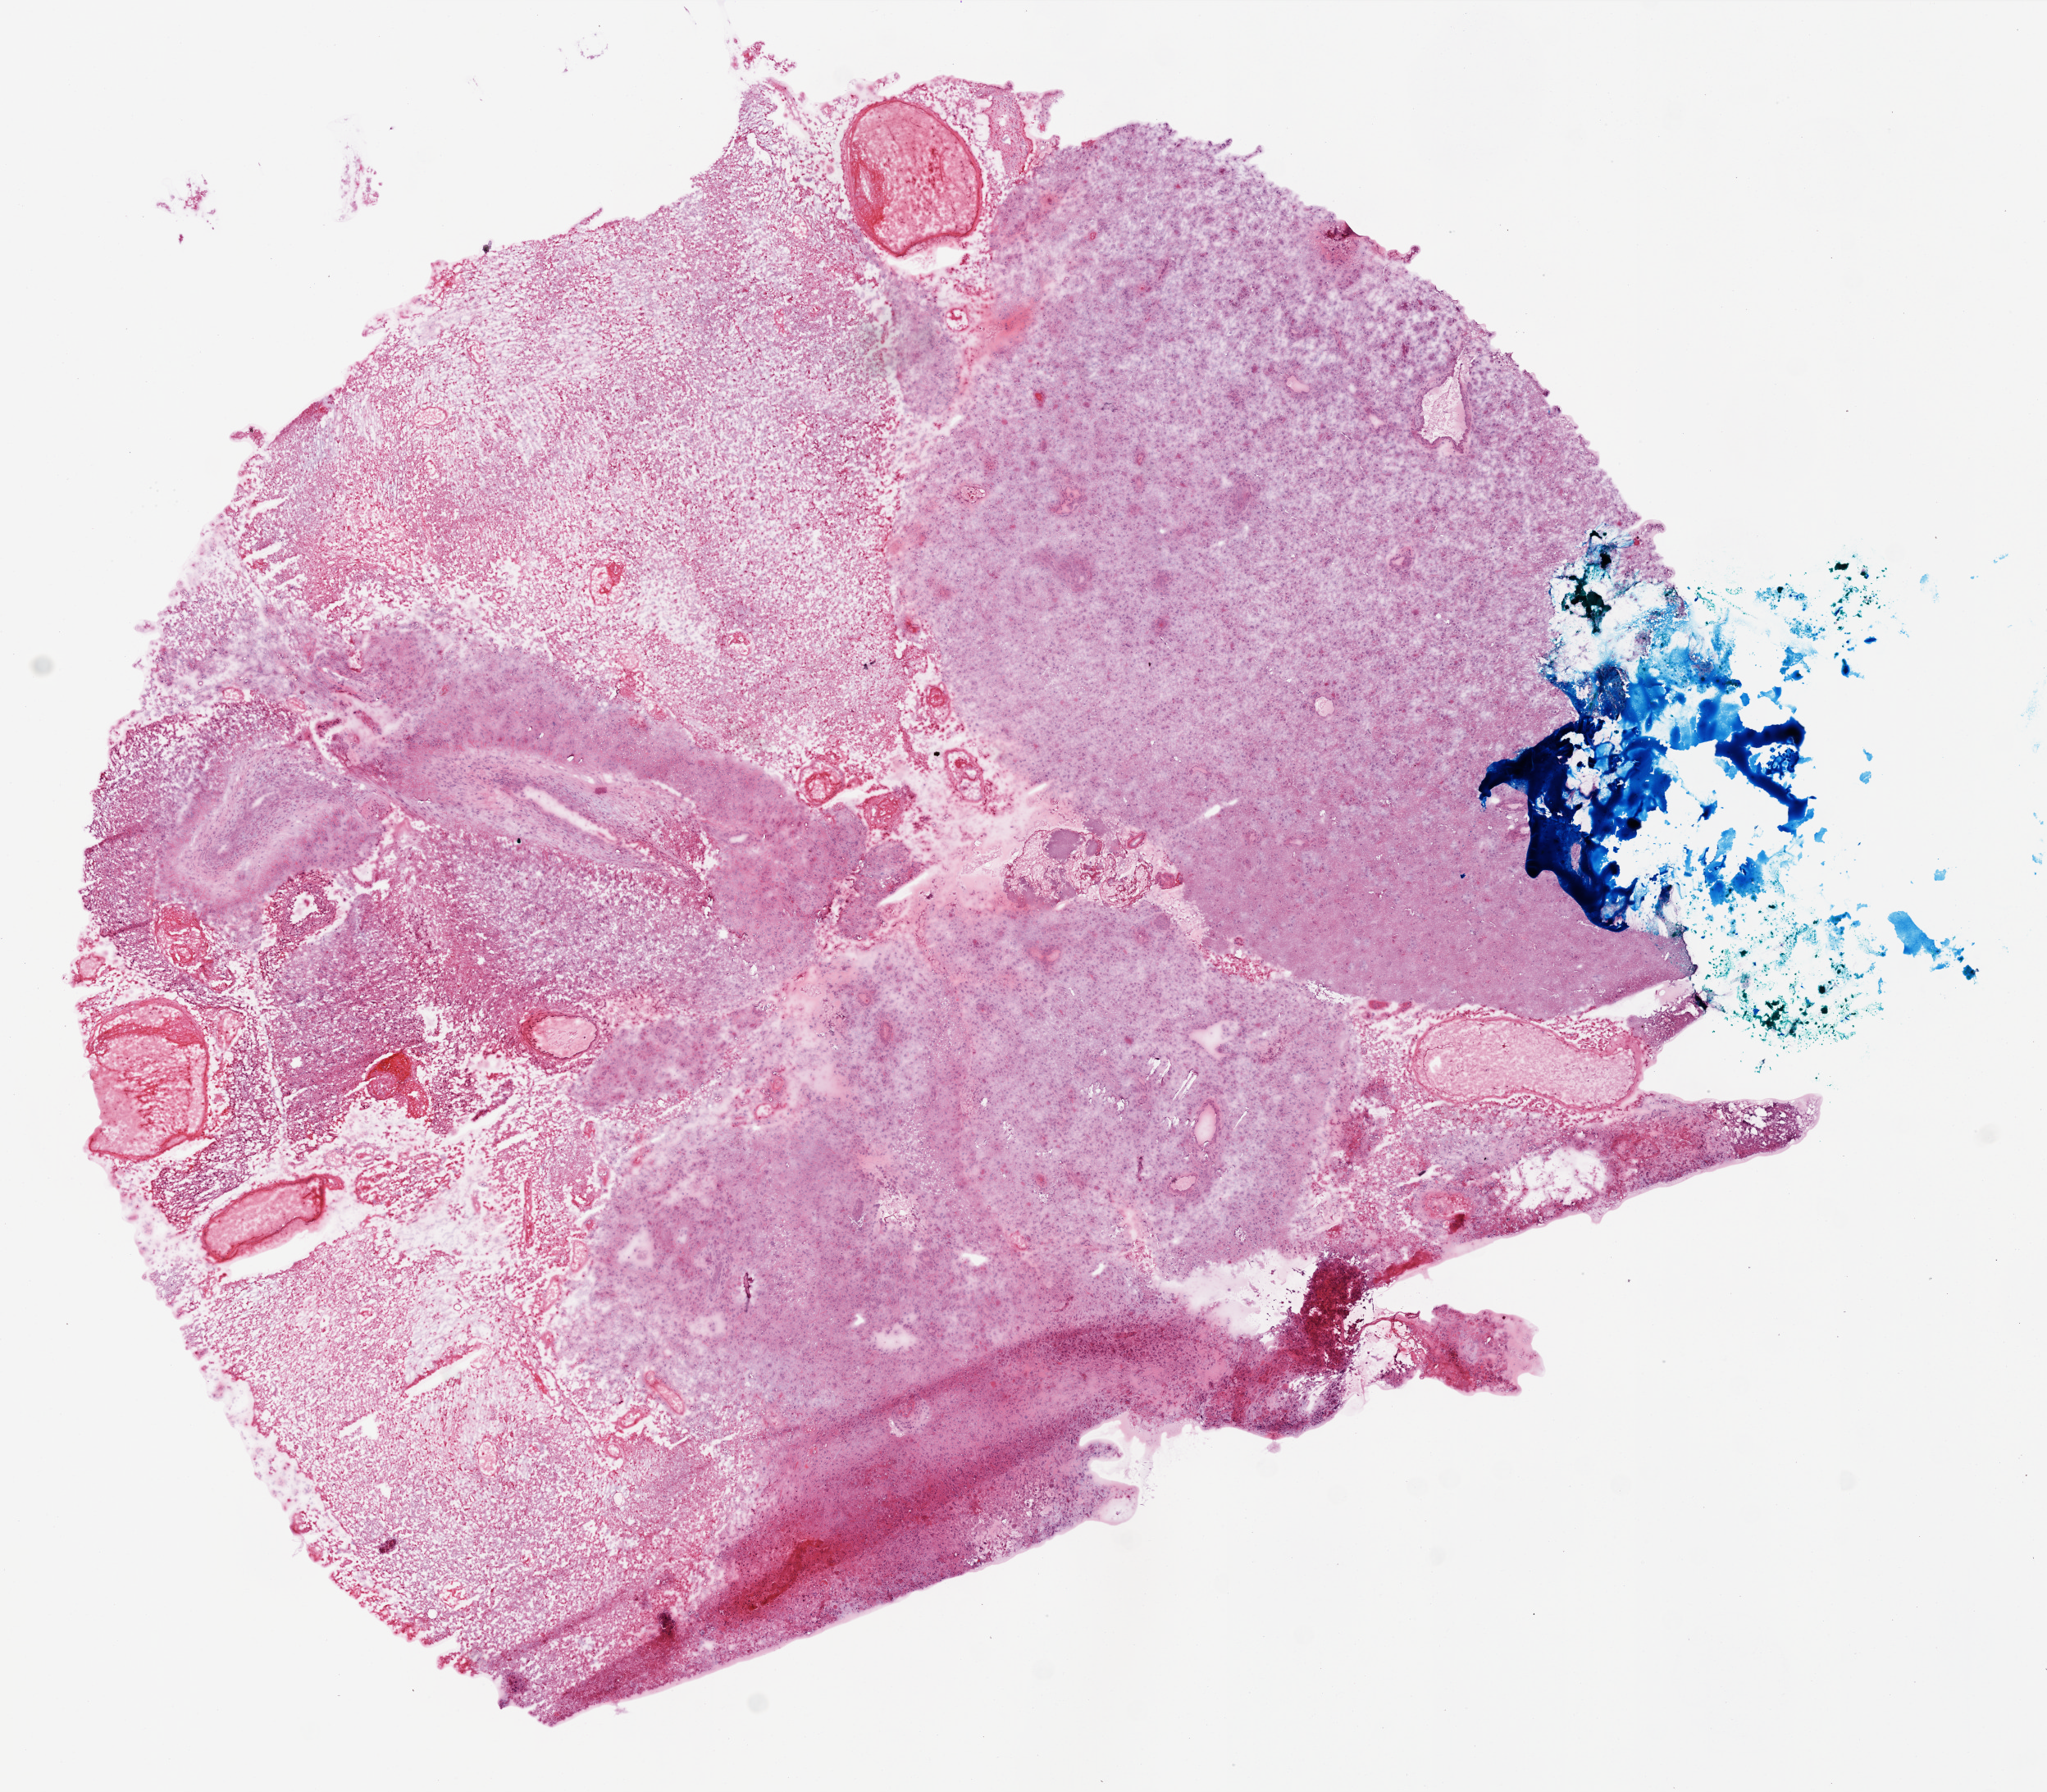
Digitized H&E-stained tissue section (whole slide), low-resolution overview of the scanned area, about 10.0 x 8.7 mm (acquisition: 20x scan), frozen section from the top of the tissue portion, brain, primary tumour sample. Male patient; age at initial diagnosis 69 years. Composition of this section per pathologist review: tumour cells 40%, tumour nuclei 90%, normal cells 0%, stromal cells 10%, necrosis 50%.
- histologic diagnosis: Glioblastoma